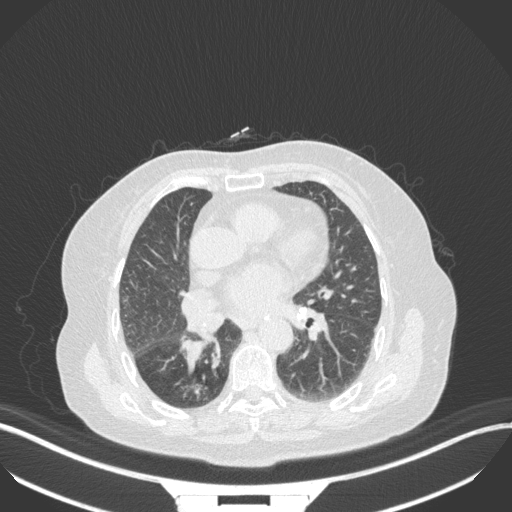
Chest CT, one axial slice; slice 152 of 329 in the series (ordered by position); 120 kVp; lung window (W 1500 / L -600 HU); 512 × 512 image matrix. Patient: female, 75 years. Case-level facts recorded for this patient, not image findings: clinical TNM (as recorded): T1b N0 M1a; histopathological grade: G1.
Outlined on this slice (rectangle marked by the reading radiologist):
- lung tumour (recorded histology: squamous cell carcinoma): bounding box (x1, y1, x2, y2) in pixels: (178, 336, 207, 374)